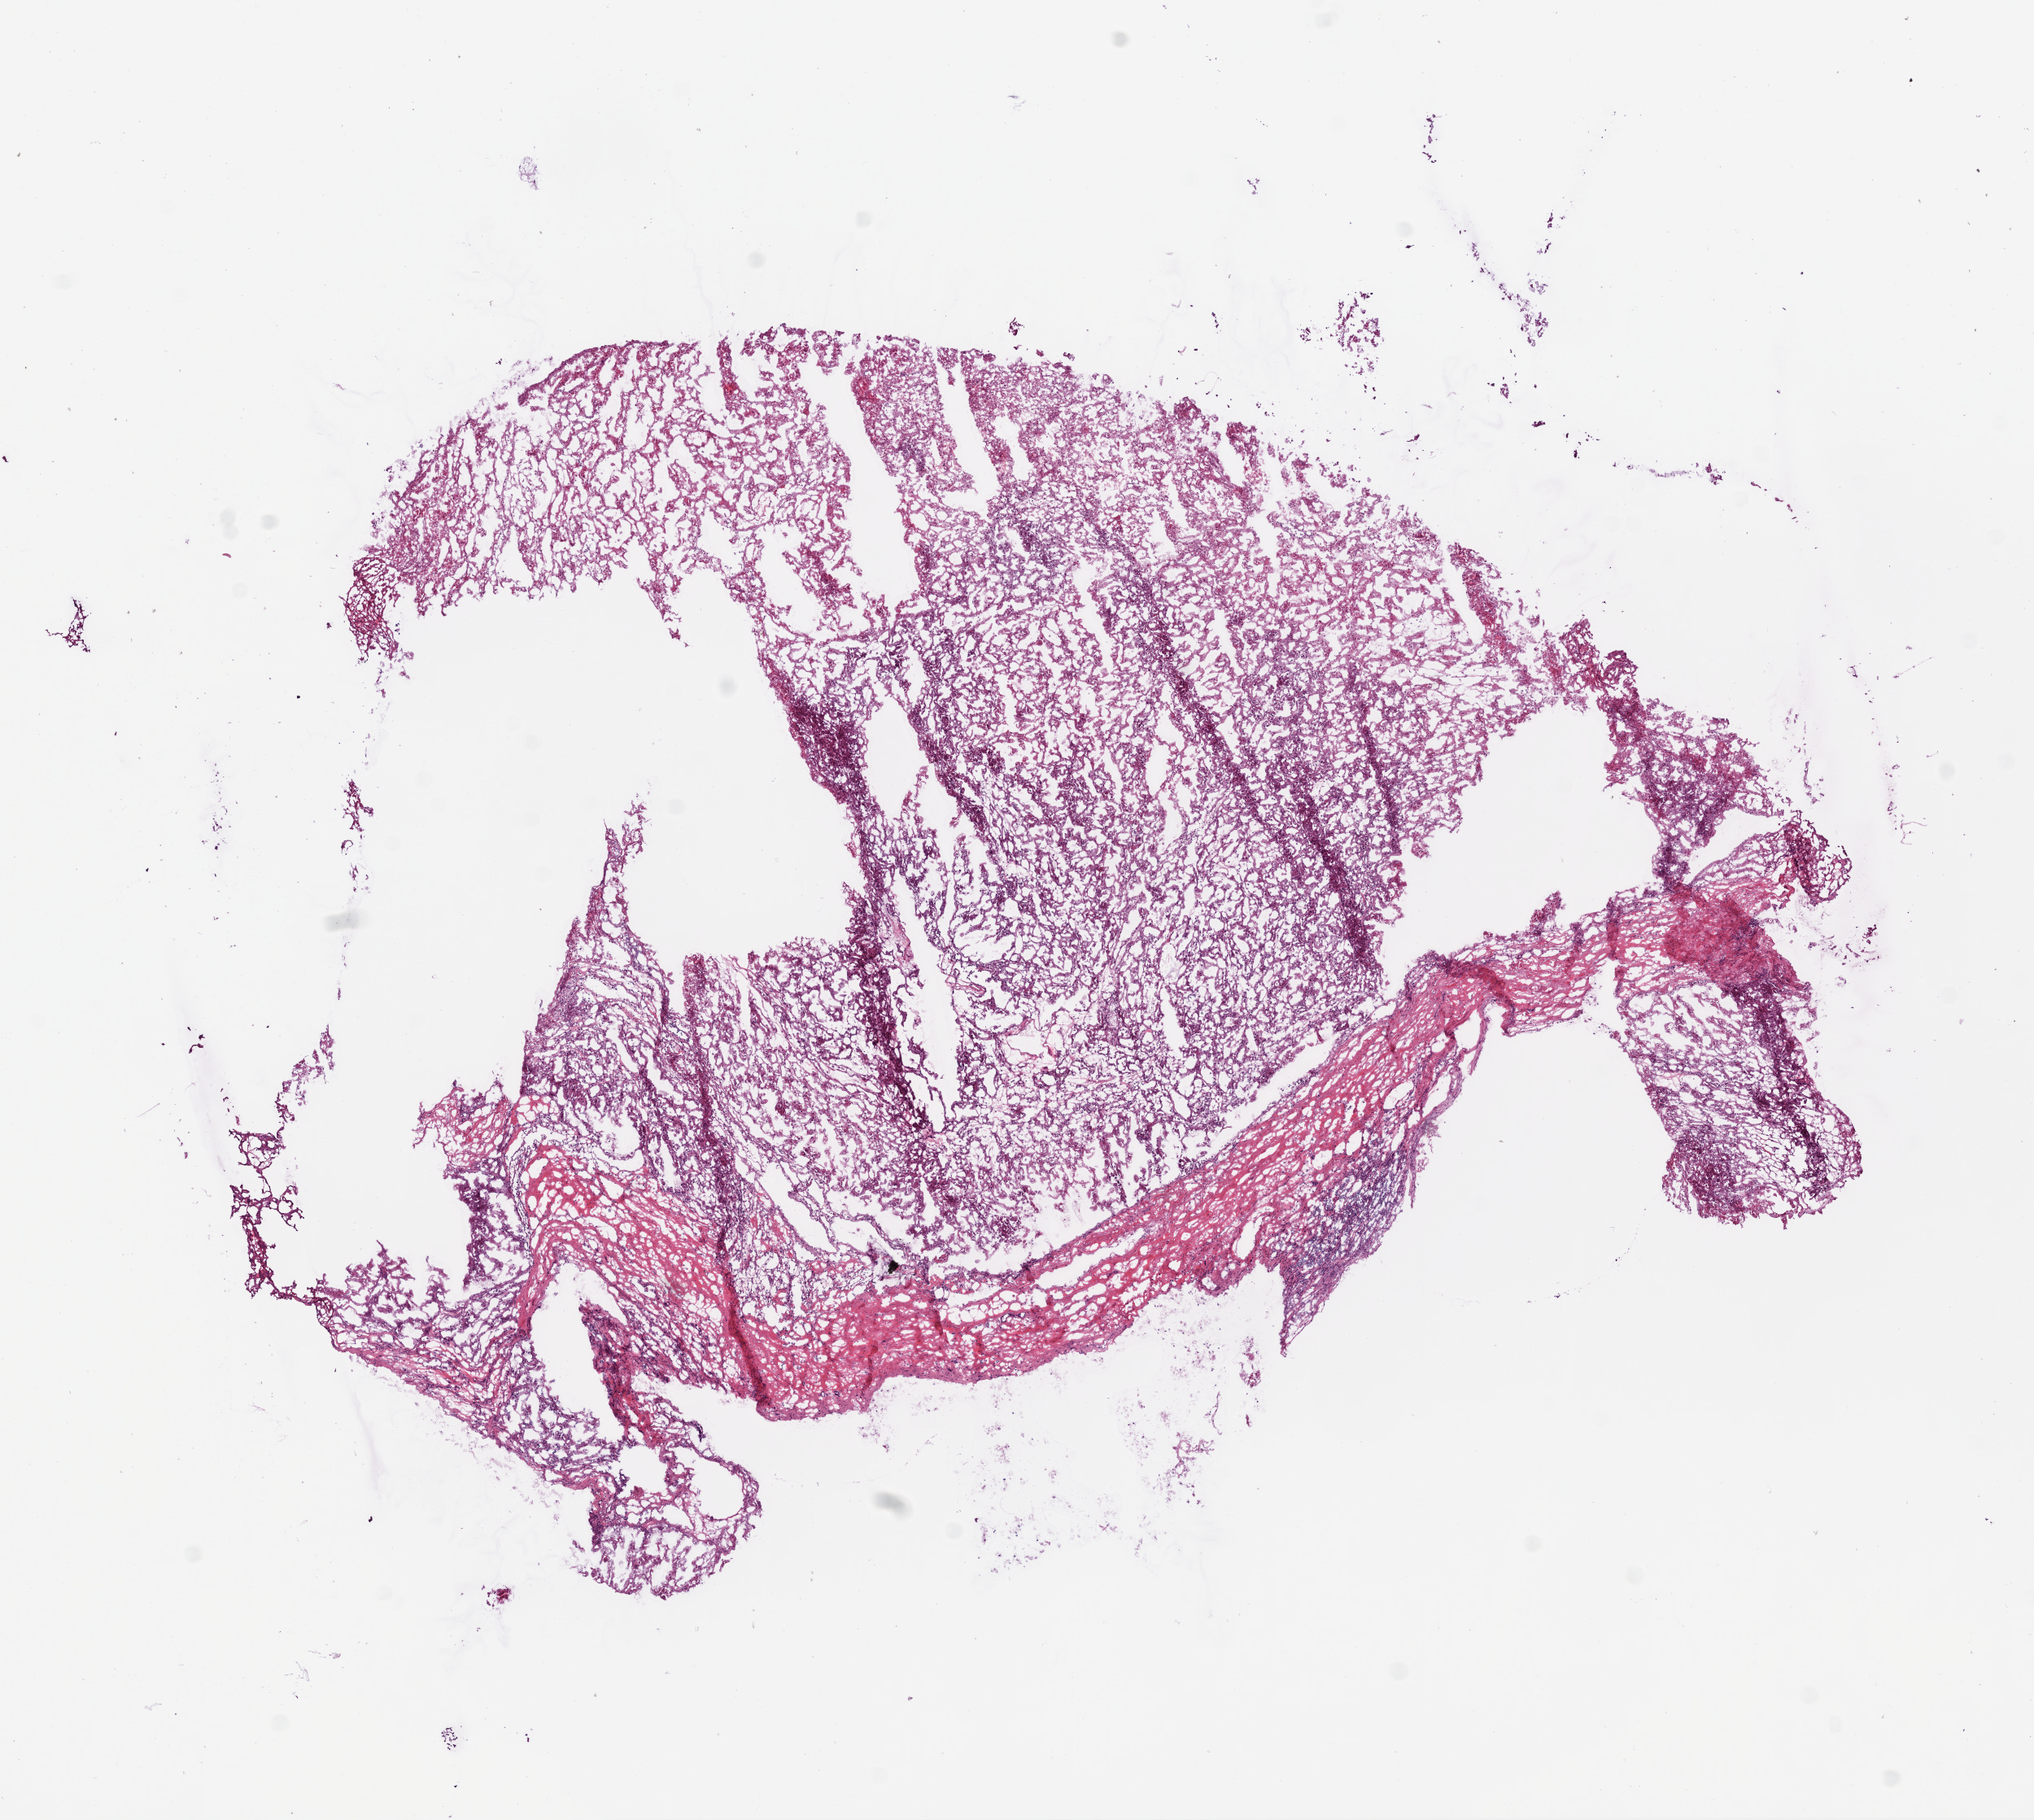
H&E-stained whole-slide image — shown as a low-resolution overview of the whole scanned area (about 10.0 x 9.0 mm, acquisition: 20x scan), frozen section, sample: primary tumour, kidney. Male patient; age at initial diagnosis 48 years. Histologic grade: G3 (poorly differentiated). Slide review estimates, as recorded: tumour cells 85%, tumour nuclei 80%, normal cells 0%, stromal cells 15%, necrosis 0%.
• AJCC pathologic stage: II (6th edition)
• pathologic diagnosis: Clear cell adenocarcinoma, NOS
• laterality: left
• lymph nodes positive (case pathology): 0 of 16 examined